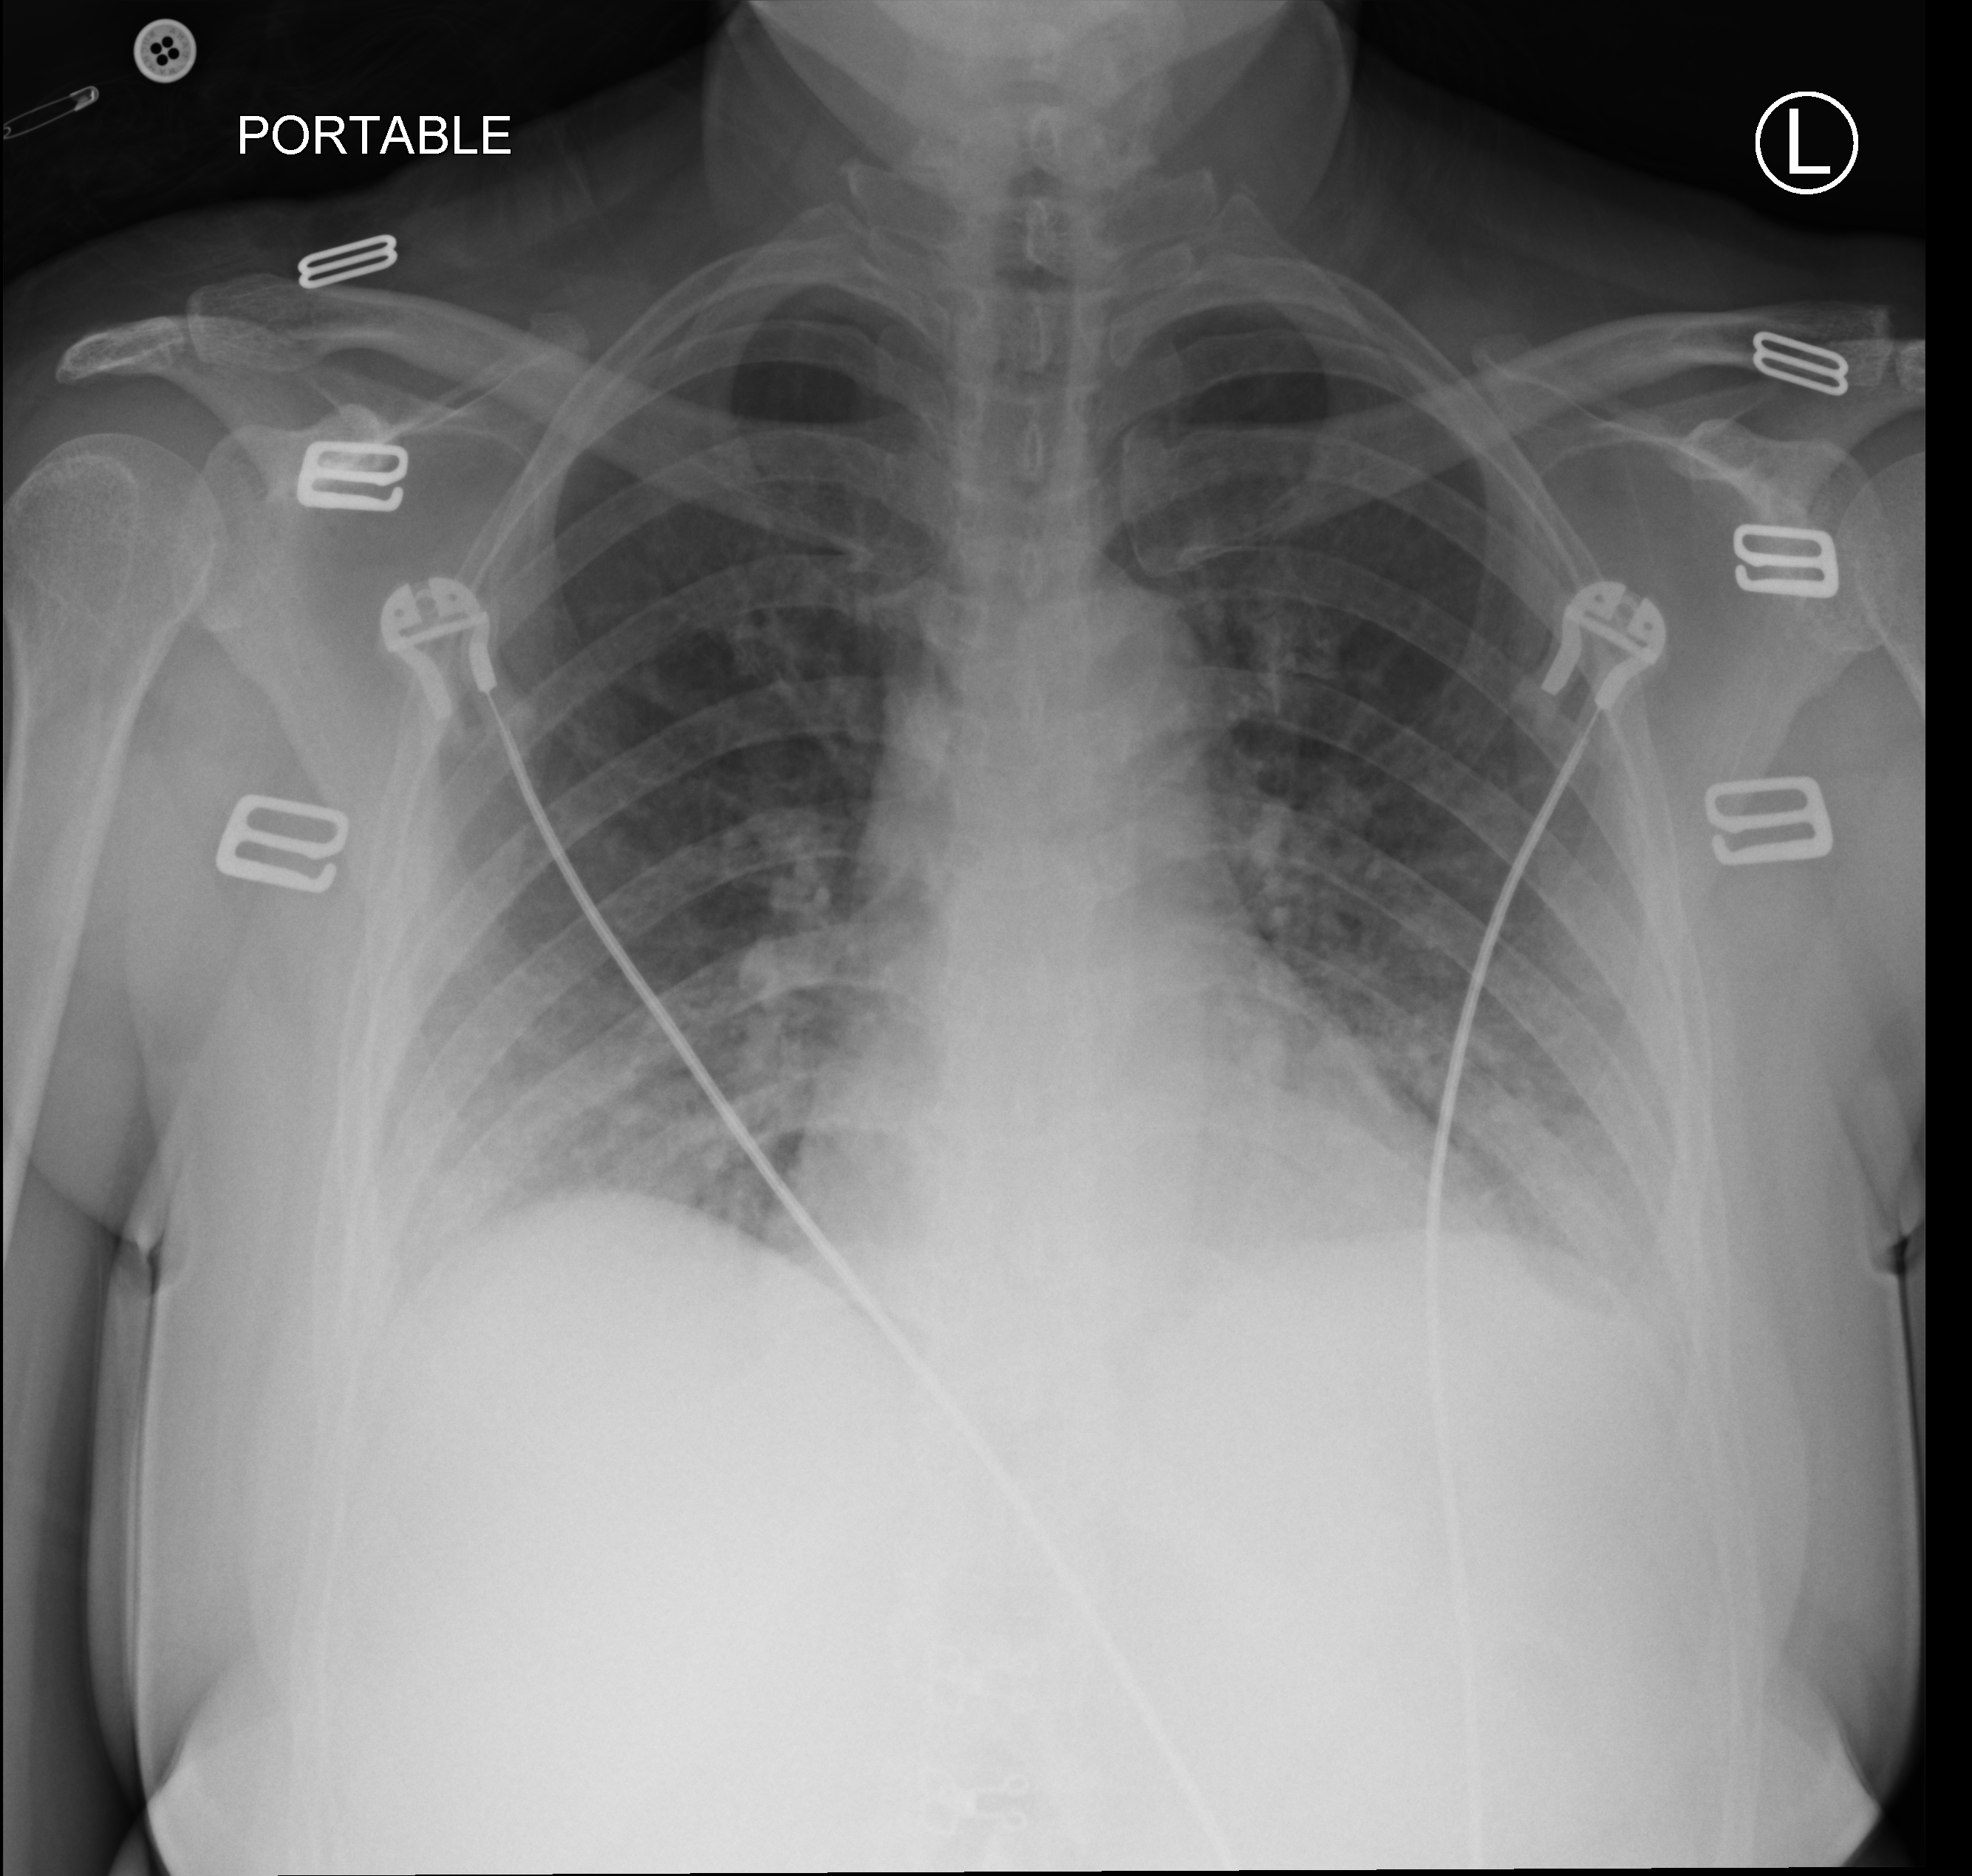
Bedside chest radiograph (computed radiography); anteroposterior (AP) projection. Female patient hospitalised with COVID-19, age 18–59 years.
Hospital-stay facts (about this admission, not read from this image; timing relative to this image not recorded):
- diabetes (admission record): no